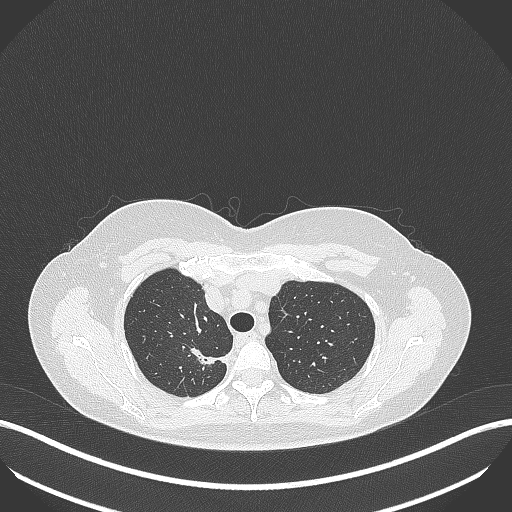
Chest CT, one axial slice; slice 317 of 386 in the series (ordered by position); lung window (W 1500 / L -600 HU); 1 mm slice thickness; 512 × 512 image matrix. Patient: female, 65 years. From the clinical record (not read from this slice): clinical TNM (as recorded): T1b N0 M0; histopathological grade: G2.
Structures marked on this image (rectangle marked by the reading radiologist):
- lung tumour (recorded histology: adenocarcinoma): box from (x=181, y=344) to (x=229, y=370) px